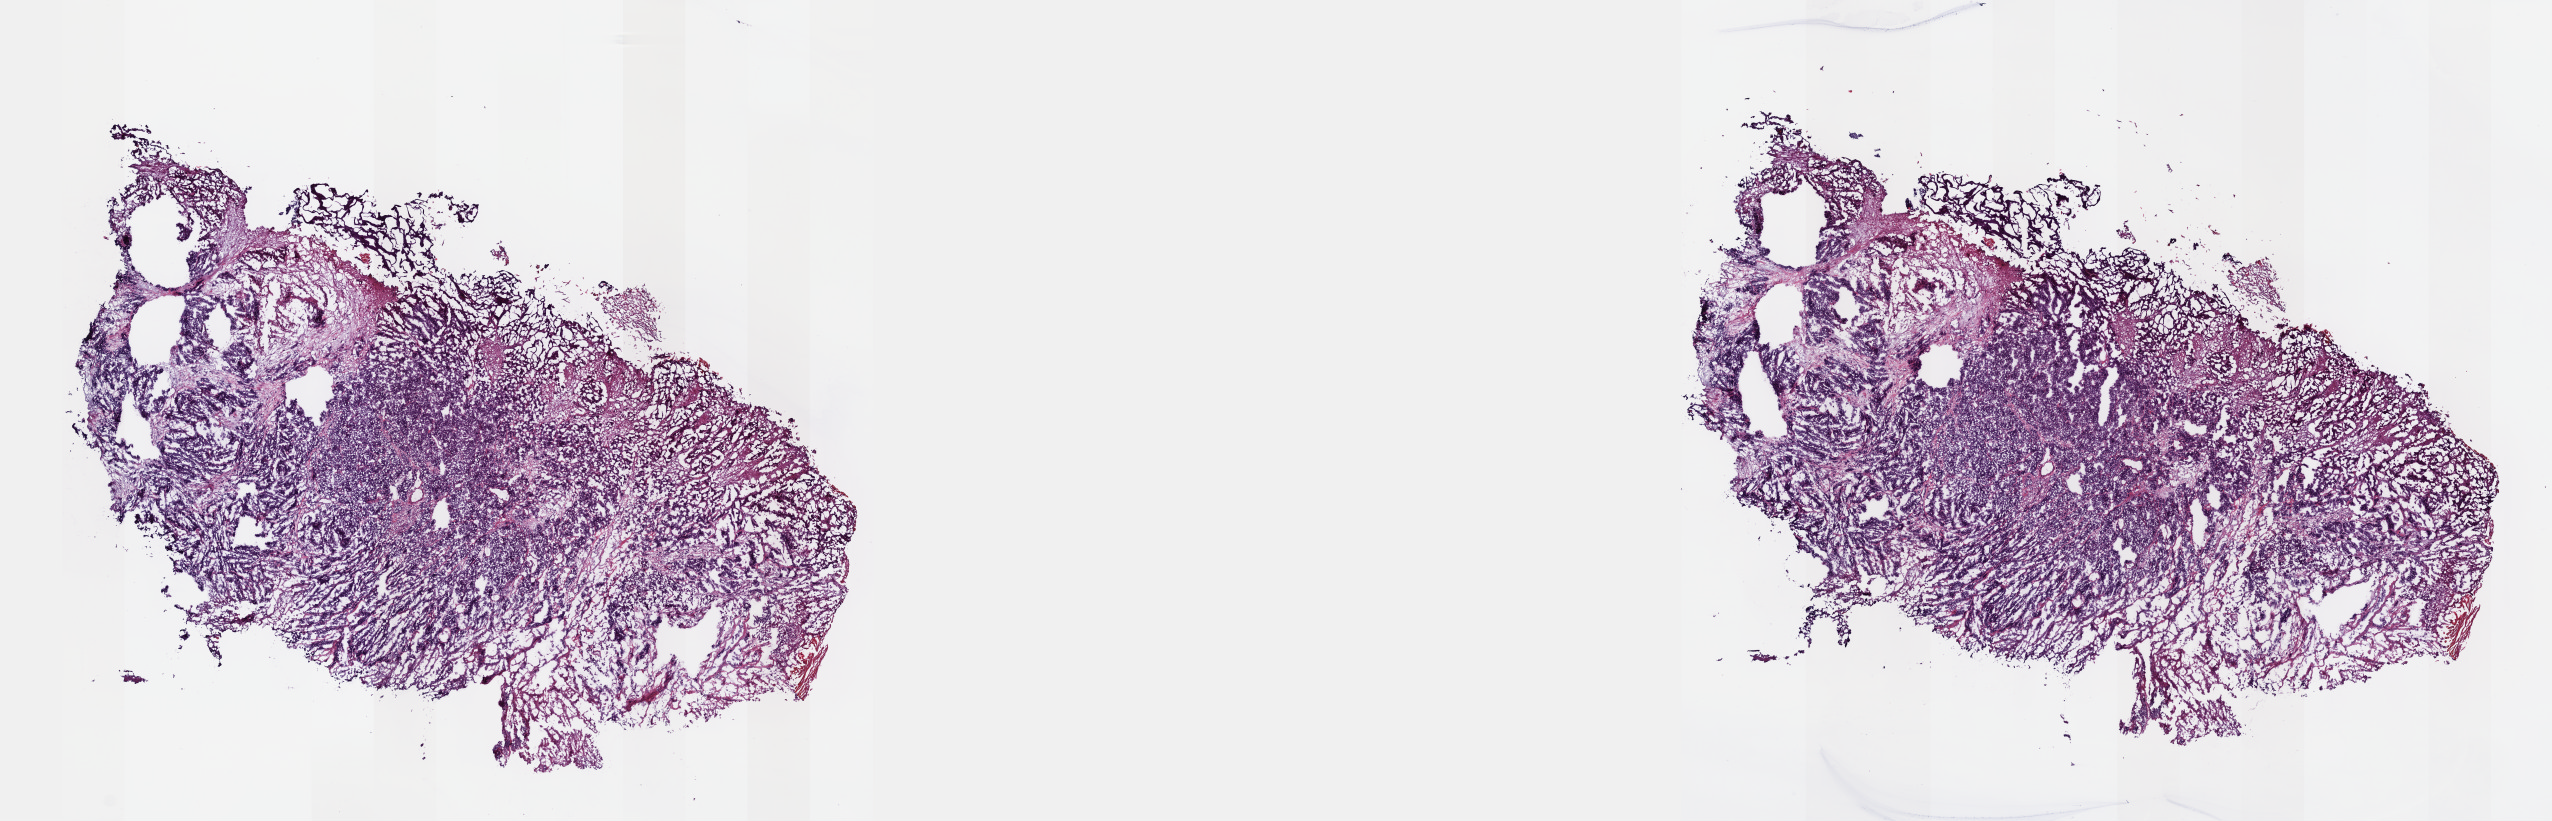
Whole-slide histology image, H&E-stained, whole scanned area (about 20.6 x 6.6 mm, acquisition: 40x scan) shown as a low-resolution overview, frozen section, sample: primary tumour, bladder. Male patient; age at initial diagnosis 71 years. Histologic grade: high grade. Slide review estimates, as recorded: tumour cells 75%, tumour nuclei 75%, normal cells 0%, stromal cells 20%, necrosis 5%. Infiltration values recorded for this section: lymphocyte infiltration 3%, monocyte infiltration 2%, neutrophil infiltration 5%.
* pathologic diagnosis: Transitional cell carcinoma
* AJCC pathologic stage: IV (7th edition)